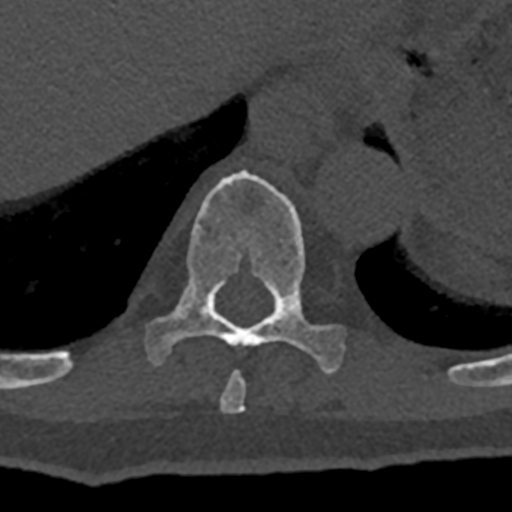
CT including the spine, one axial slice; reconstruction kernel Br40s/3; 120 kVp; bone window (W 1800 / L 400 HU); 512 × 512 image matrix, field of view 160 × 160 mm. Patient: male, 74 years. Case-level facts recorded for this patient, not image findings: primary cancer: renal; vertebrae with lytic lesions (as recorded): T10, L1, L2, L3, L4, L5.
Annotated regions visible in this slice (semi-automatic segmentation, software-assisted and operator-edited):
- T10 vertebra: bounding box [x1, y1, x2, y2] px = [70, 170, 345, 374]
- T9 vertebra: [220, 370, 246, 413]